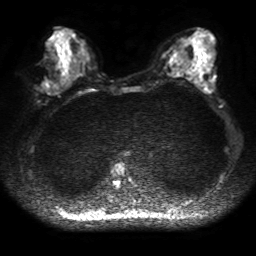
Breast MRI, one axial slice; slice 21 of 50 in the series (ordered by position); diffusion-weighted series; image 2 of 4 stored at this slice position (different b-values; order by instance number); 1.5 T; 4 mm slice thickness; 256 × 256 image matrix, field of view 320 × 320 mm. Female patient.
Outlined on this slice (outlined manually by an expert reader):
- tumour on diffusion-weighted imaging: bounding box (x1, y1, x2, y2) in pixels: (41, 80, 50, 88)